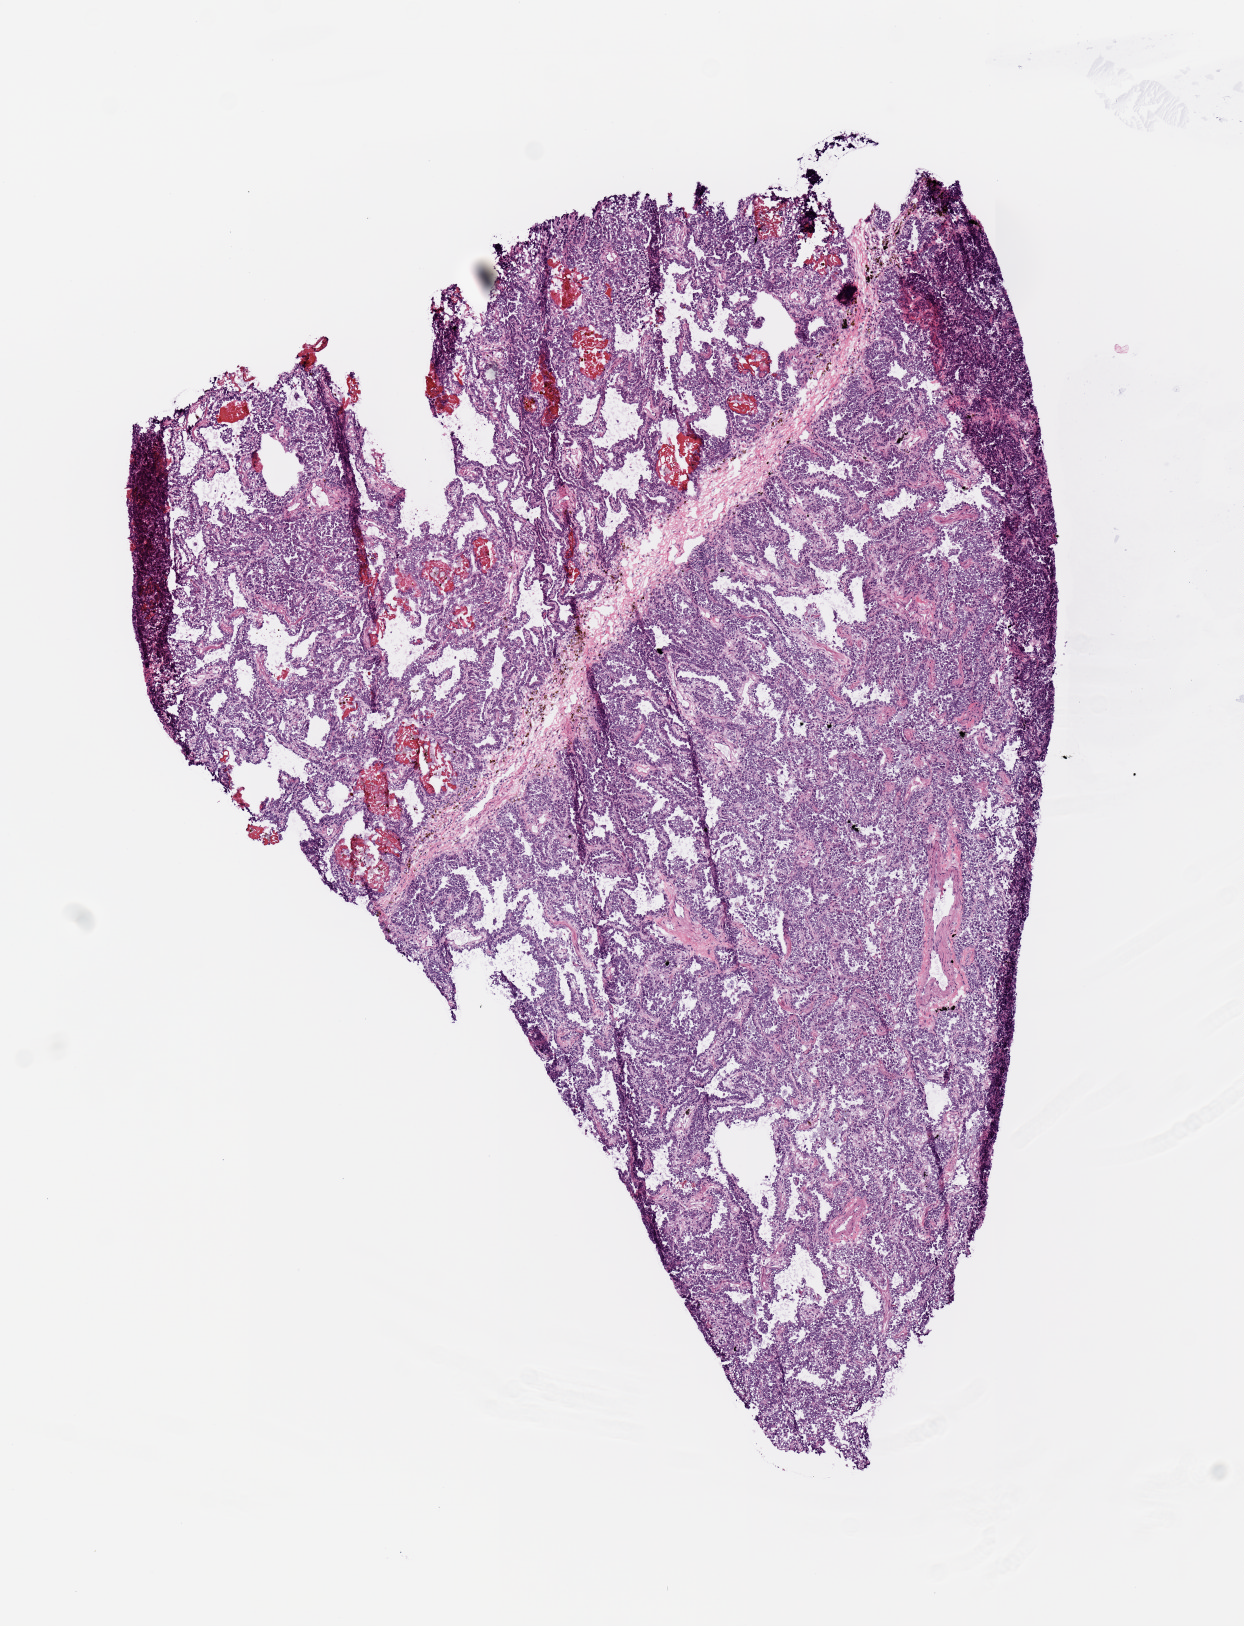
Digitized H&E tissue section (whole slide) — low-resolution overview of the scanned area, about 4.9 x 6.4 mm, frozen section from the top of the tissue portion, sample: primary tumour, lung. Male, age 72 years at initial diagnosis. Composition of this section per pathologist review: tumour cells 85%, tumour nuclei 85%, normal cells 0%, stromal cells 10%, necrosis 5%. Infiltration values recorded for this section: lymphocyte infiltration 5%.
• histologic diagnosis: Papillary adenocarcinoma, NOS (upper lobe, lung)
• AJCC pathologic stage: IB (6th edition)